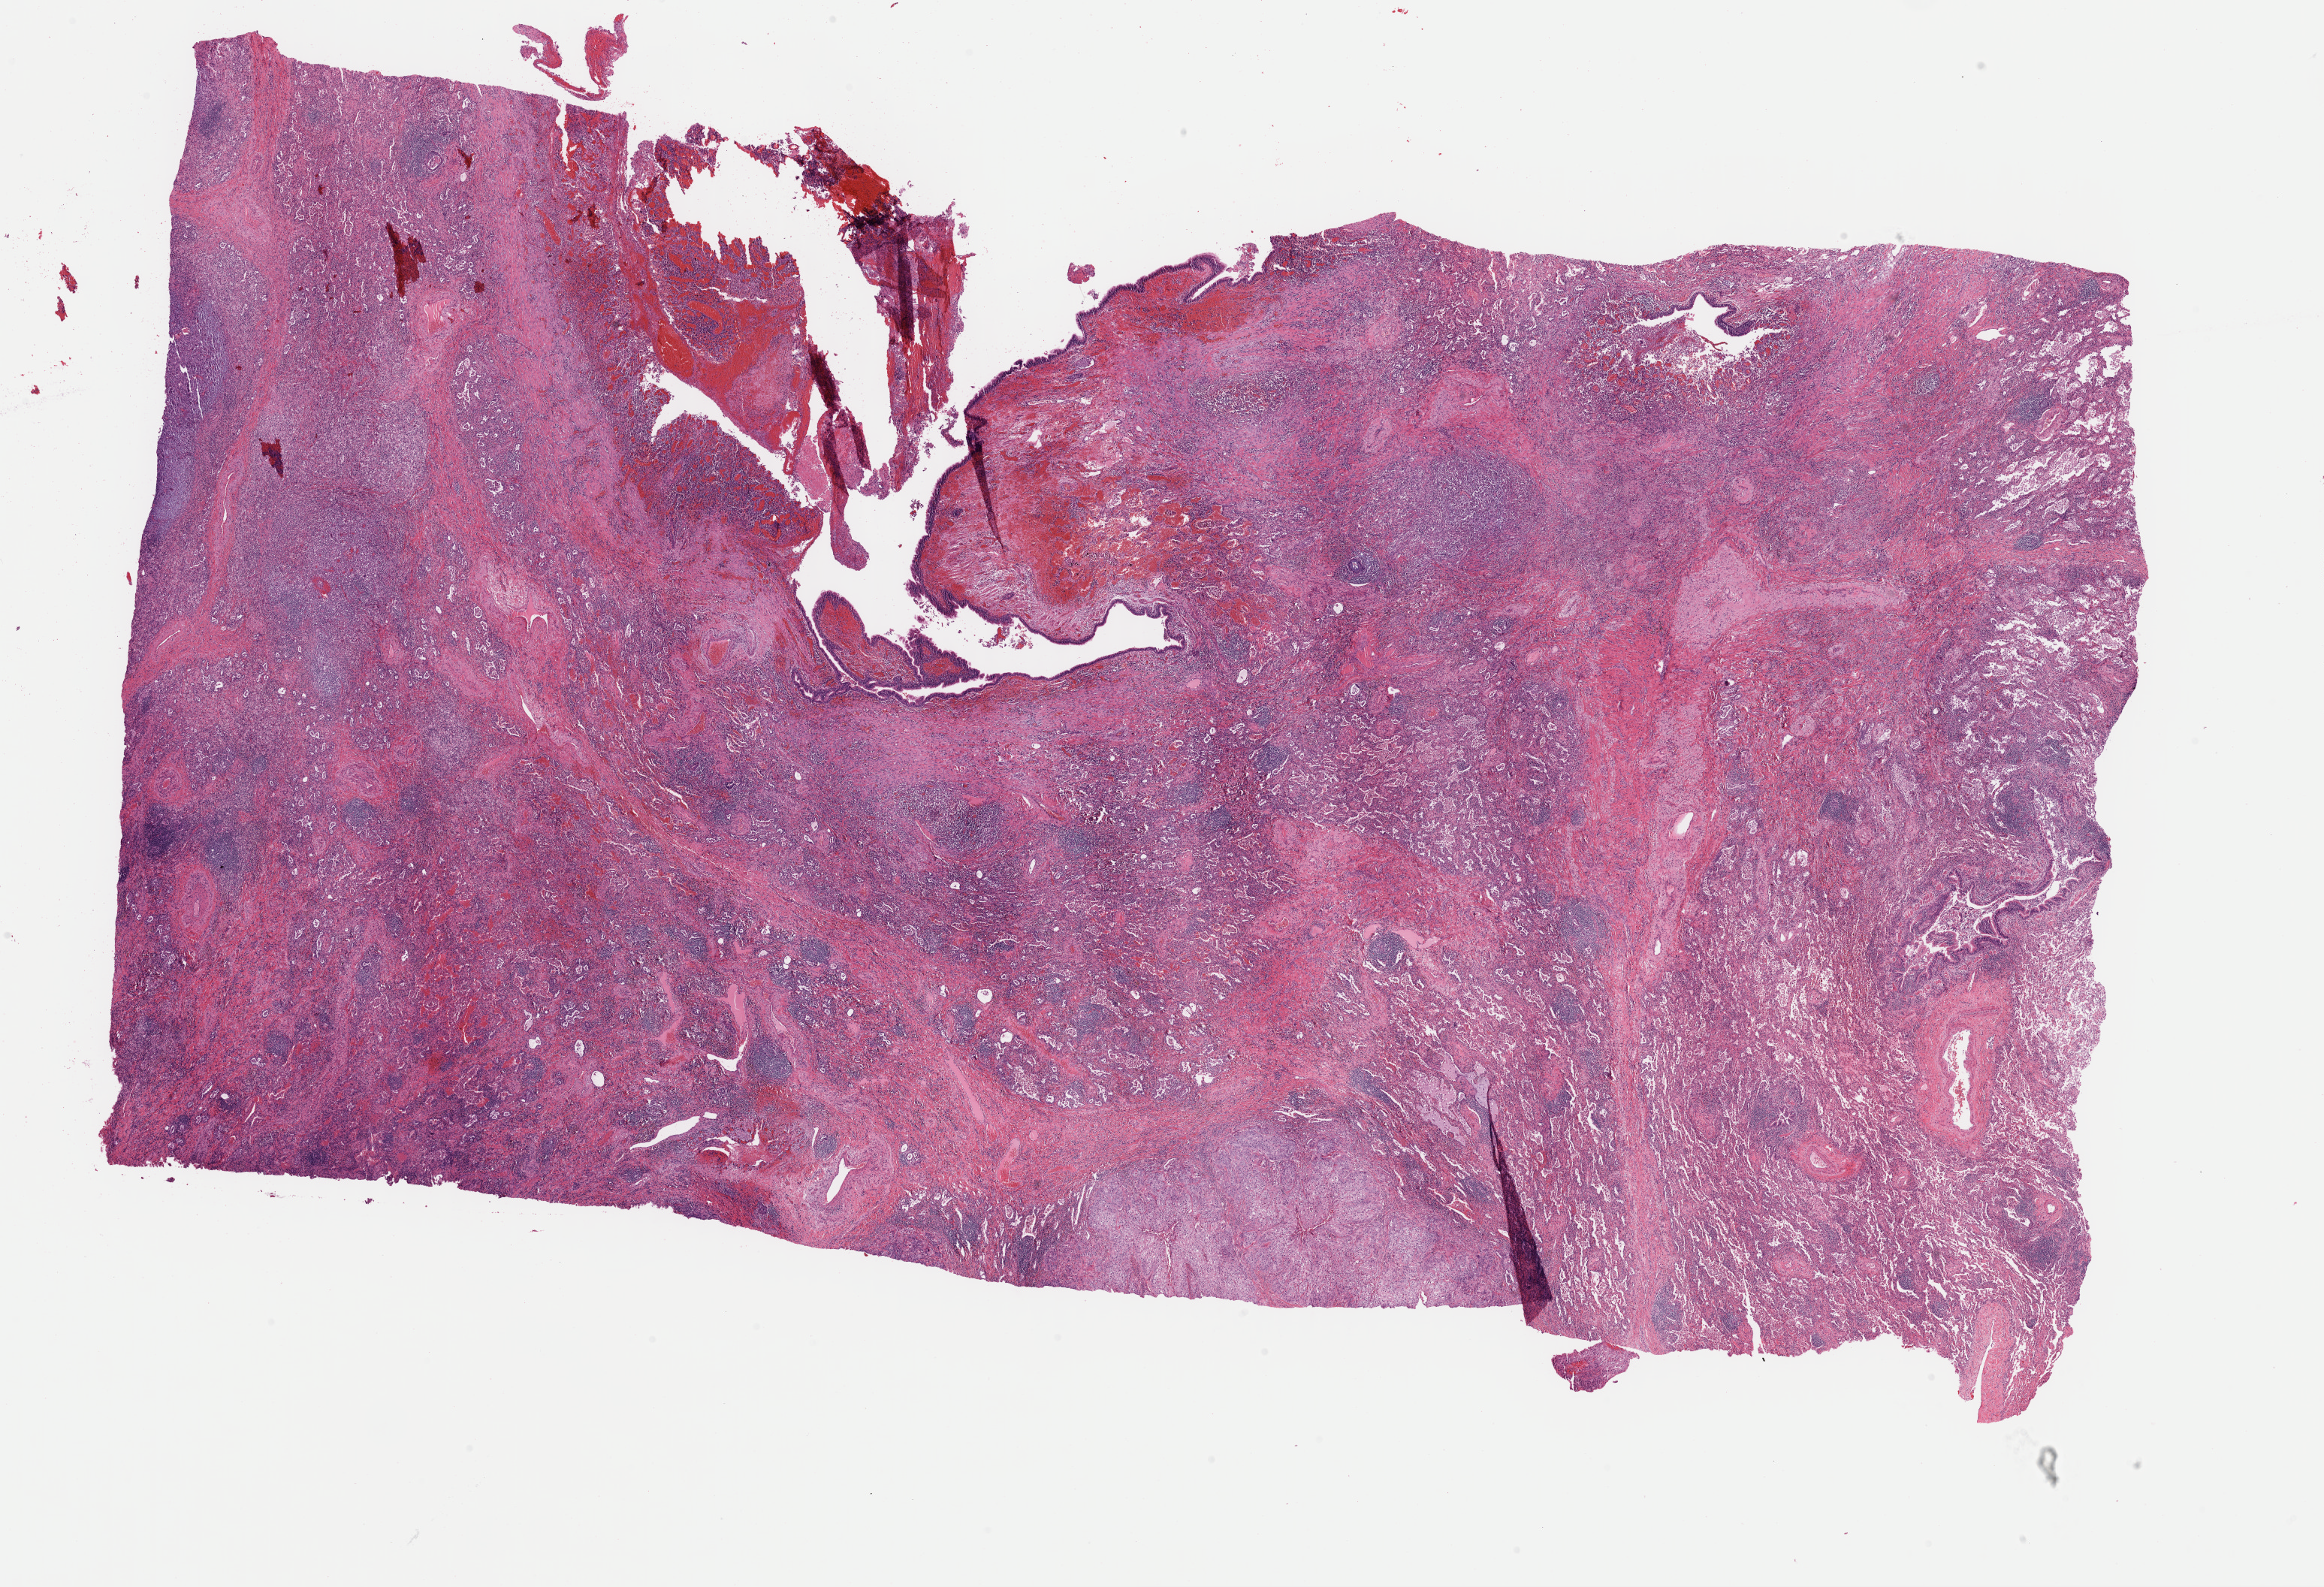
Whole-slide histology image, H&E, low-resolution overview of the scanned area, about 24.4 x 16.7 mm (acquisition: 40x scan), FFPE section, primary tumour sample from the lung. Female, age 73 years at initial diagnosis.
- pathologic diagnosis: Squamous cell carcinoma, NOS (lower lobe, lung)
- AJCC pathologic stage: IIIA